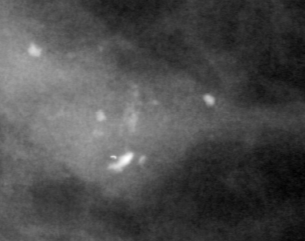
Crop from a digitized film mammogram around one marked abnormality; right breast; MLO view.
Calcifications, morphology pleomorphic, distribution clustered; BI-RADS assessment category 4; subtlety rating 5 on a 1 (subtle) to 5 (obvious) scale; pathology (as recorded): malignant.